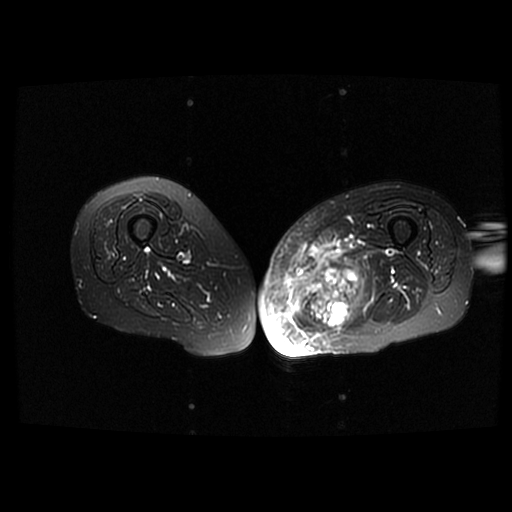
MRI of an extremity soft-tissue mass, one axial slice; slice 36 of 42 in the series (ordered by position); T2-weighted fat-saturated; 6 mm slice thickness; 512 × 512 image matrix, field of view 420 × 420 mm. Female patient. From the clinical record (not read from this slice): histological type: pleomorphic leiomyosarcoma; grade: high; site of the primary tumour: left thigh.
Structures marked on this image (outlined manually by an expert reader):
- gross tumour volume including surrounding oedema: box from (x=288, y=240) to (x=367, y=330) px
- gross tumour volume (mass): (x=298, y=263)–(x=364, y=330)